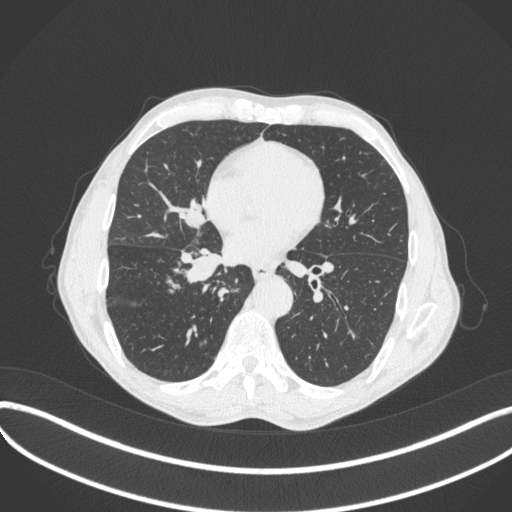
Chest CT, one axial slice; reconstruction kernel B31f; lung window (W 1500 / L -600 HU); 1 mm slice thickness; 512 × 512 image matrix, field of view 400 × 400 mm. Patient: male, 65 years. Case-level facts recorded for this patient, not image findings: clinical TNM (as recorded): T2a N0 M0.
Structures marked on this image (bounding box drawn by a radiologist):
- lung tumour (recorded histology: squamous cell carcinoma): box from (x=176, y=246) to (x=228, y=284) px